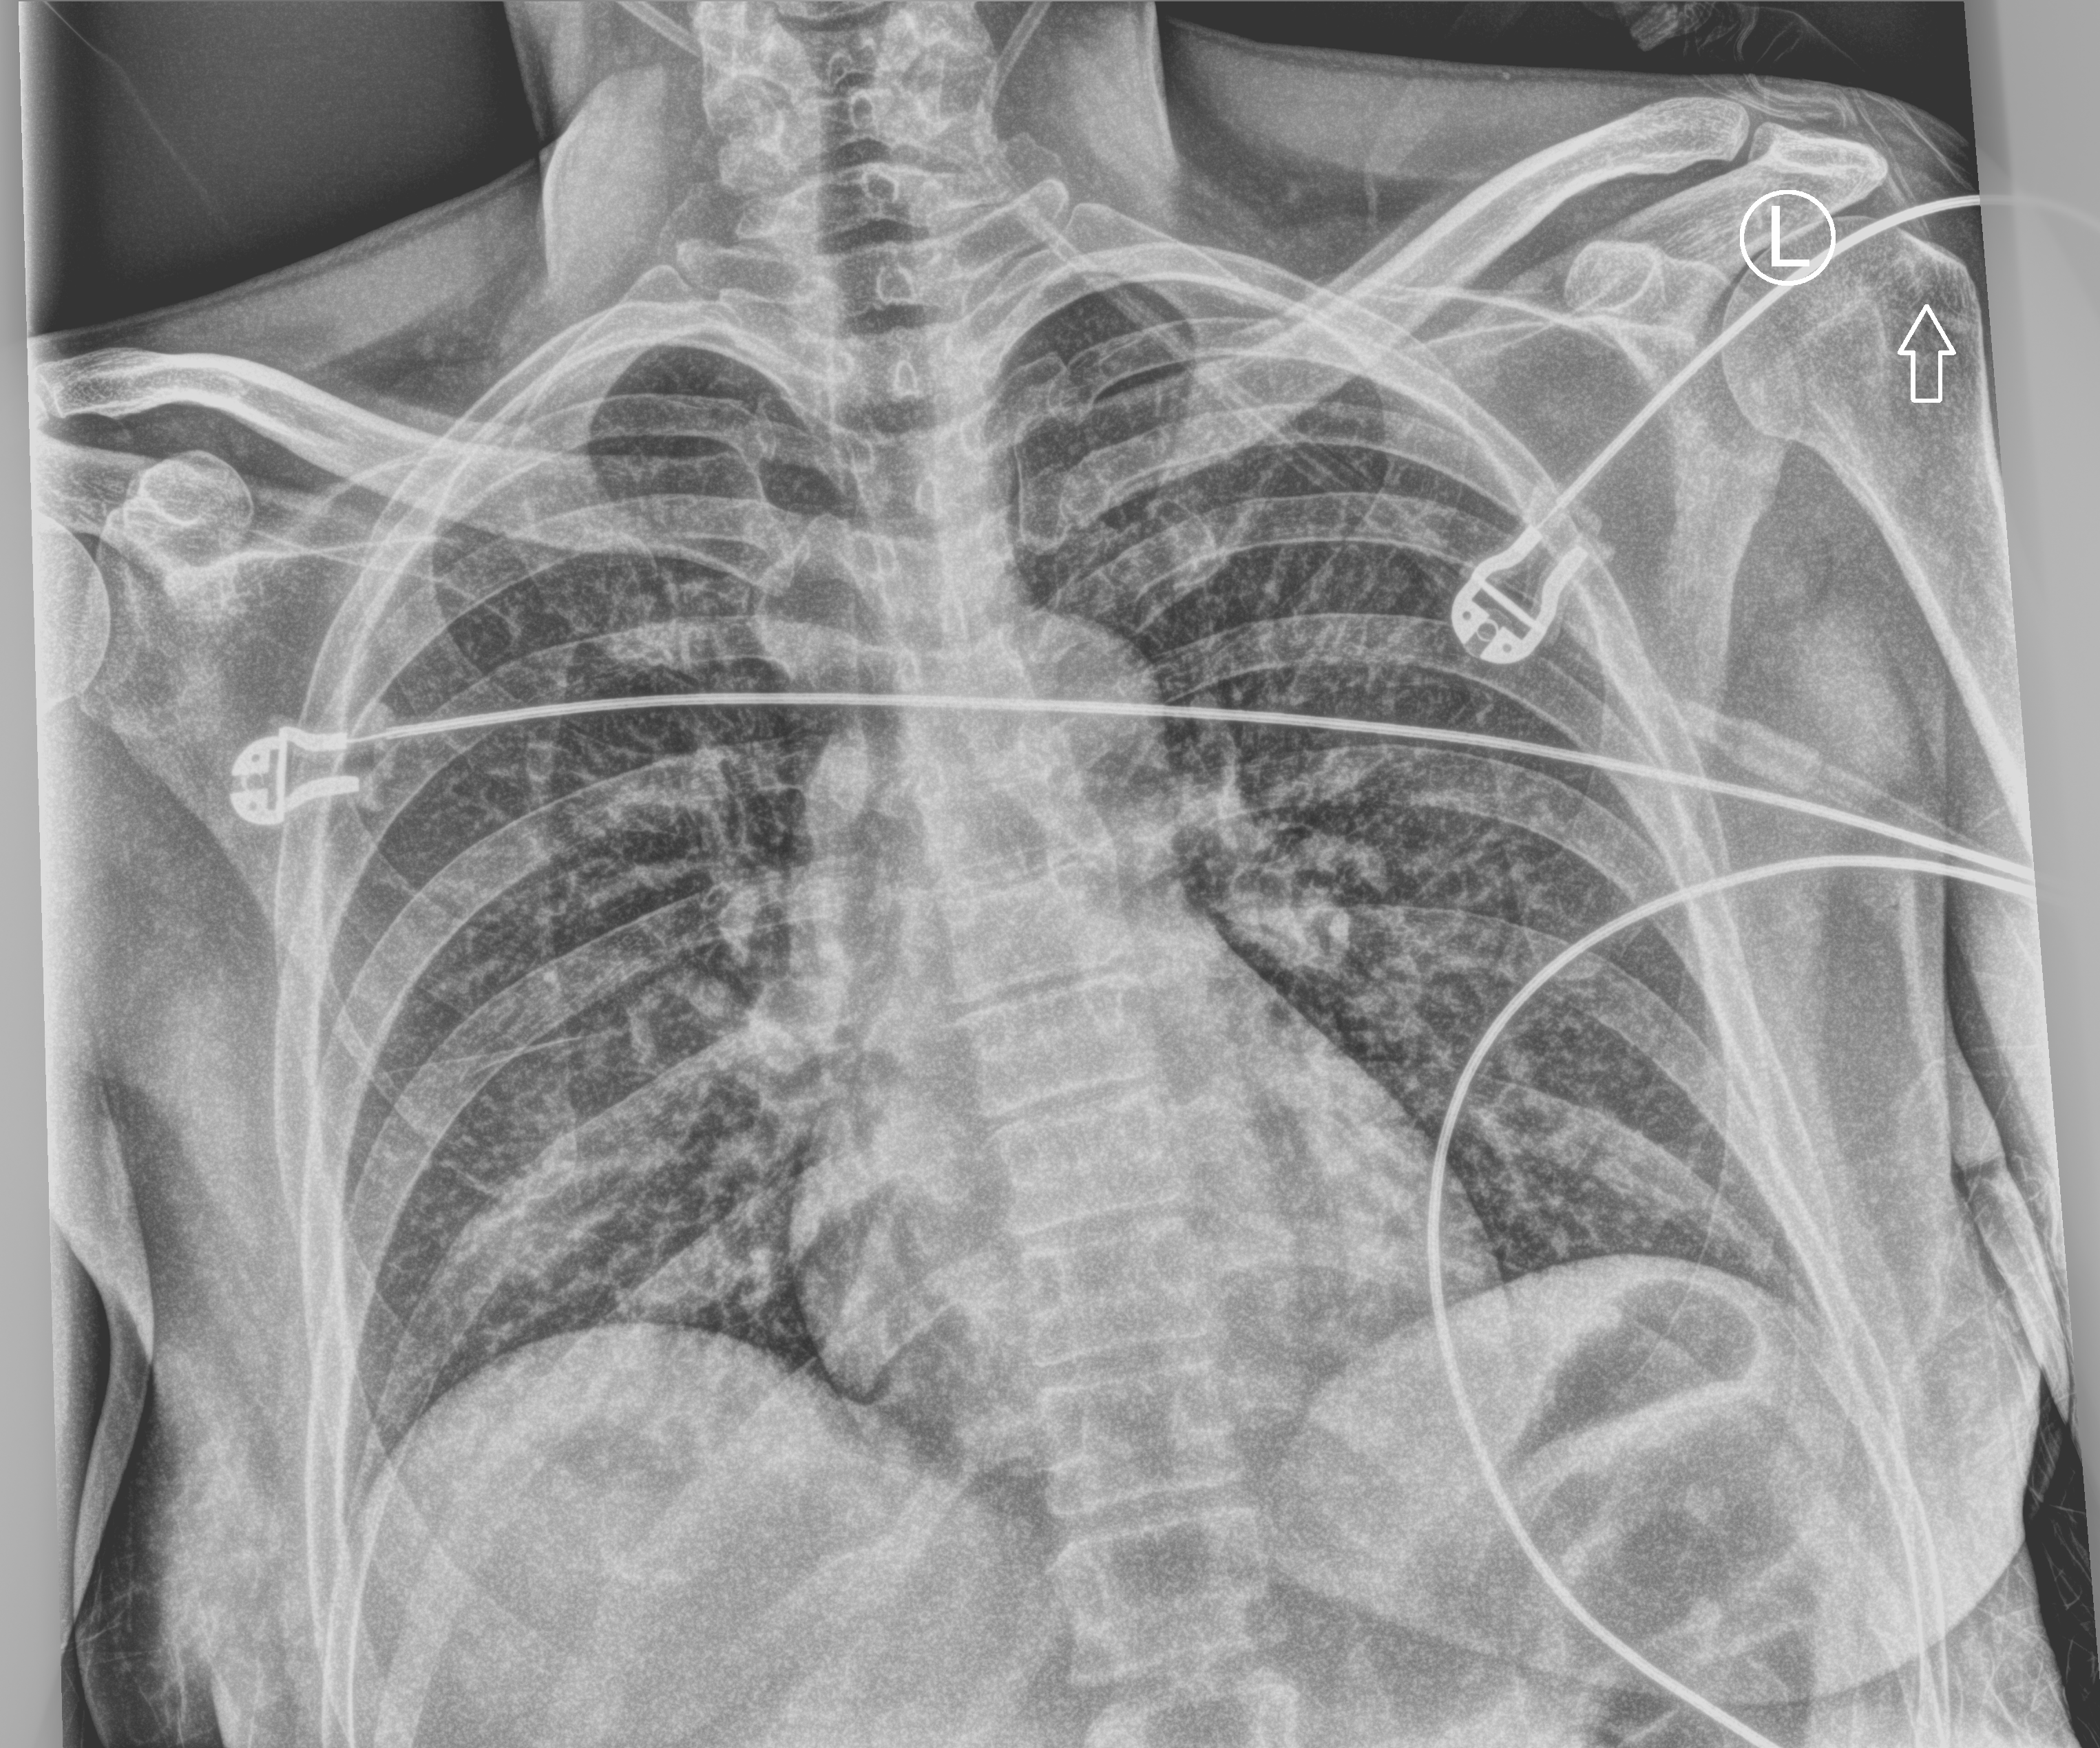
Bedside chest radiograph (computed radiography), anteroposterior (AP) projection. Female patient hospitalised with COVID-19, age 18–59 years.
From the hospital-stay record, not from the radiograph (when in the stay this image was taken is not recorded): length of hospital stay: 27 days.